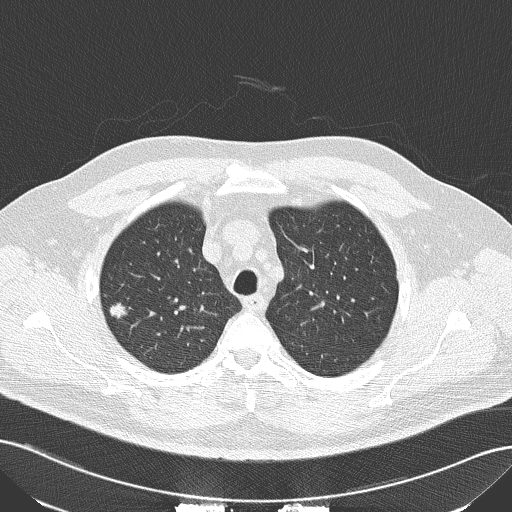
Low-dose screening chest CT, axial slice, second annual screen, lung window (W 1500 / L -600 HU), 2 mm slice thickness, 120 kVp, slice 34 of 152 in the series. Male, age 56 years at enrolment. Current smoker at enrolment.
Expert-annotated lung lesion, box from (x=96, y=291) to (x=143, y=332) px. Screening reader's record for this exam (one nodule recorded; not confirmed to be the boxed lesion): non-calcified nodule or mass ≥4 mm, right upper lobe, 10 × 9 mm, spiculated (stellate) margins, soft tissue attenuation, pre-existing on the prior screen: no. Official screen result: positive, other. Participant outcome: lung cancer diagnosed 117 days after this screen — squamous cell carcinoma, NOS, right upper lobe, moderately differentiated (G2), stage IA (AJCC 6th edition), 10 mm at pathology.